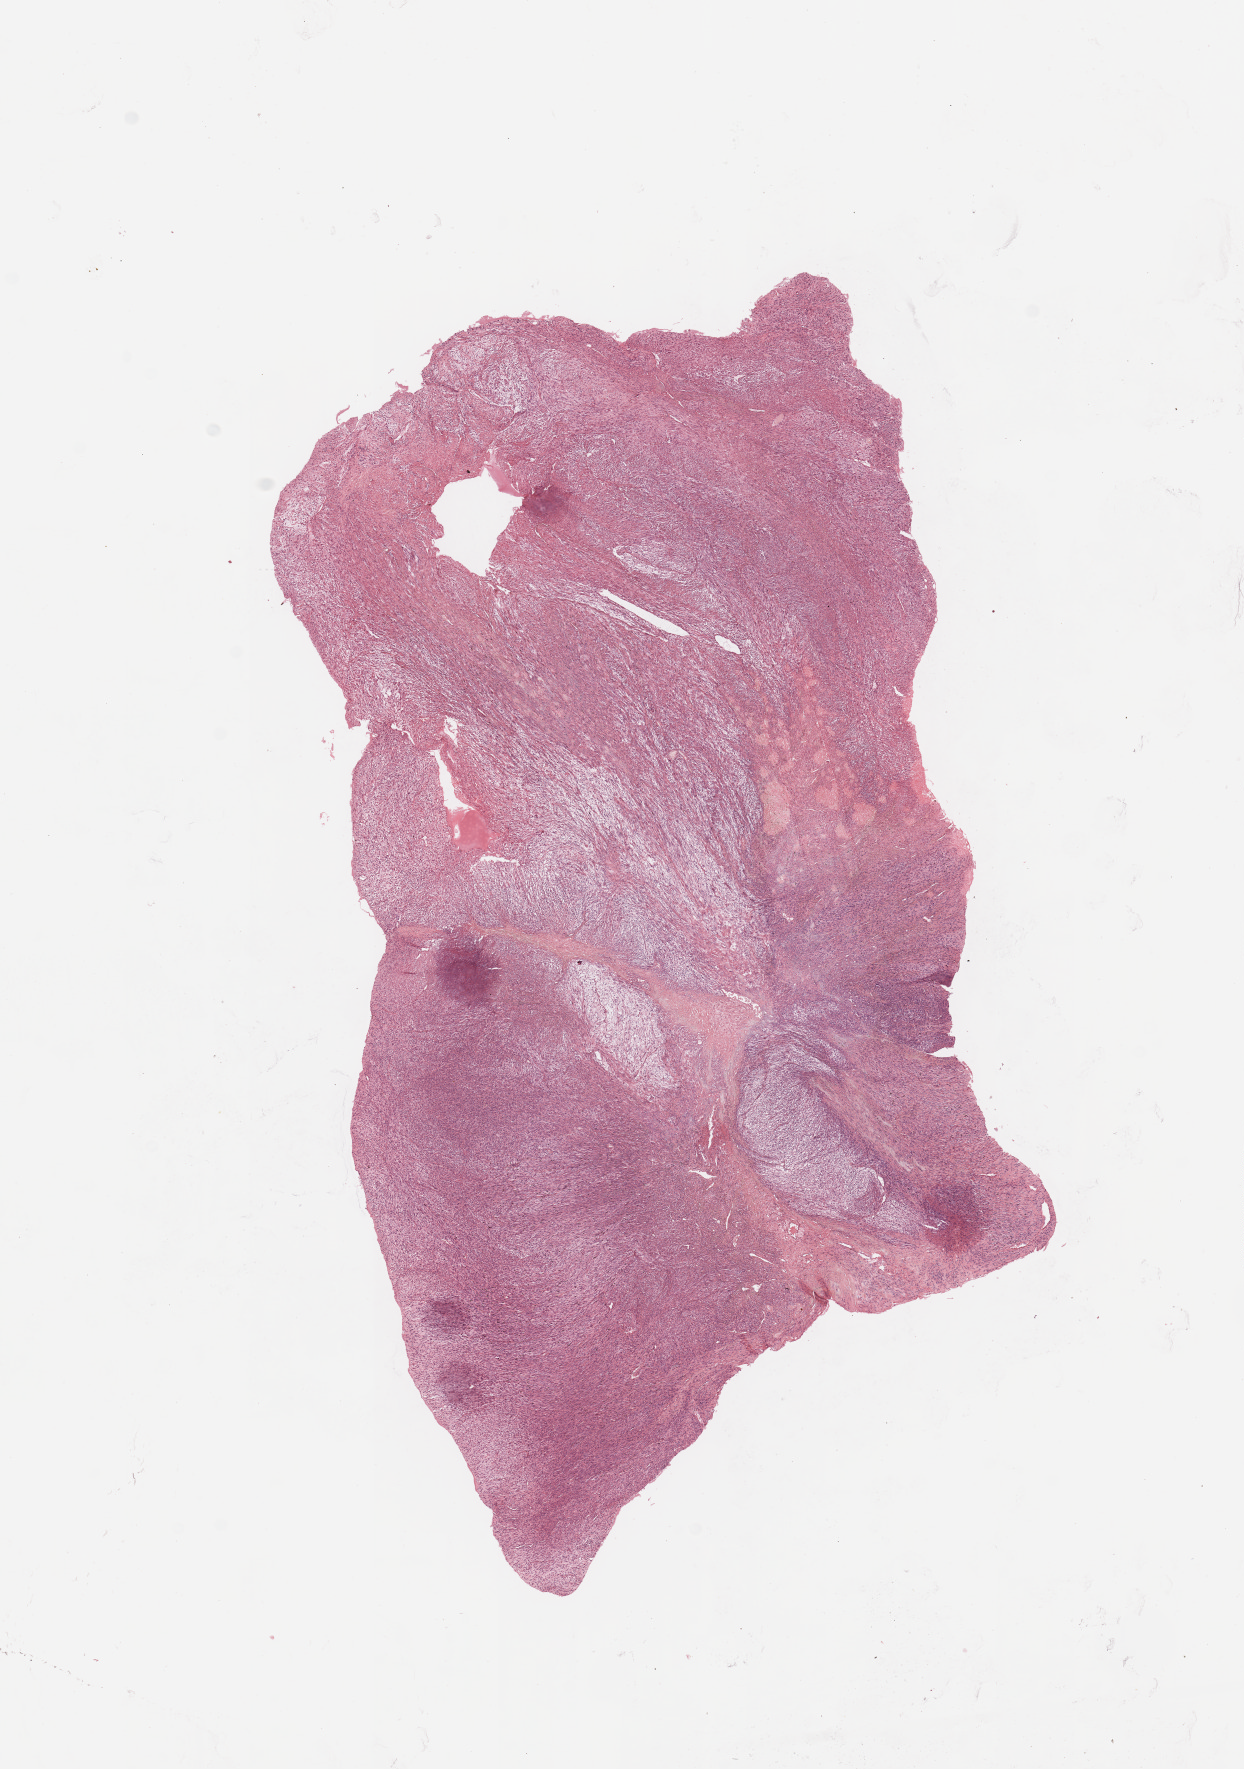
Whole-slide histology image, H&E — low-resolution overview of the scanned area, about 9.8 x 14.0 mm (acquisition: 20x scan), tumour tissue sample. Patient: male, age 66 years.
* primary tumour site (as recorded): chest
* patient diagnosis (cohort enrolment): sarcoma (site not recorded at cohort level)